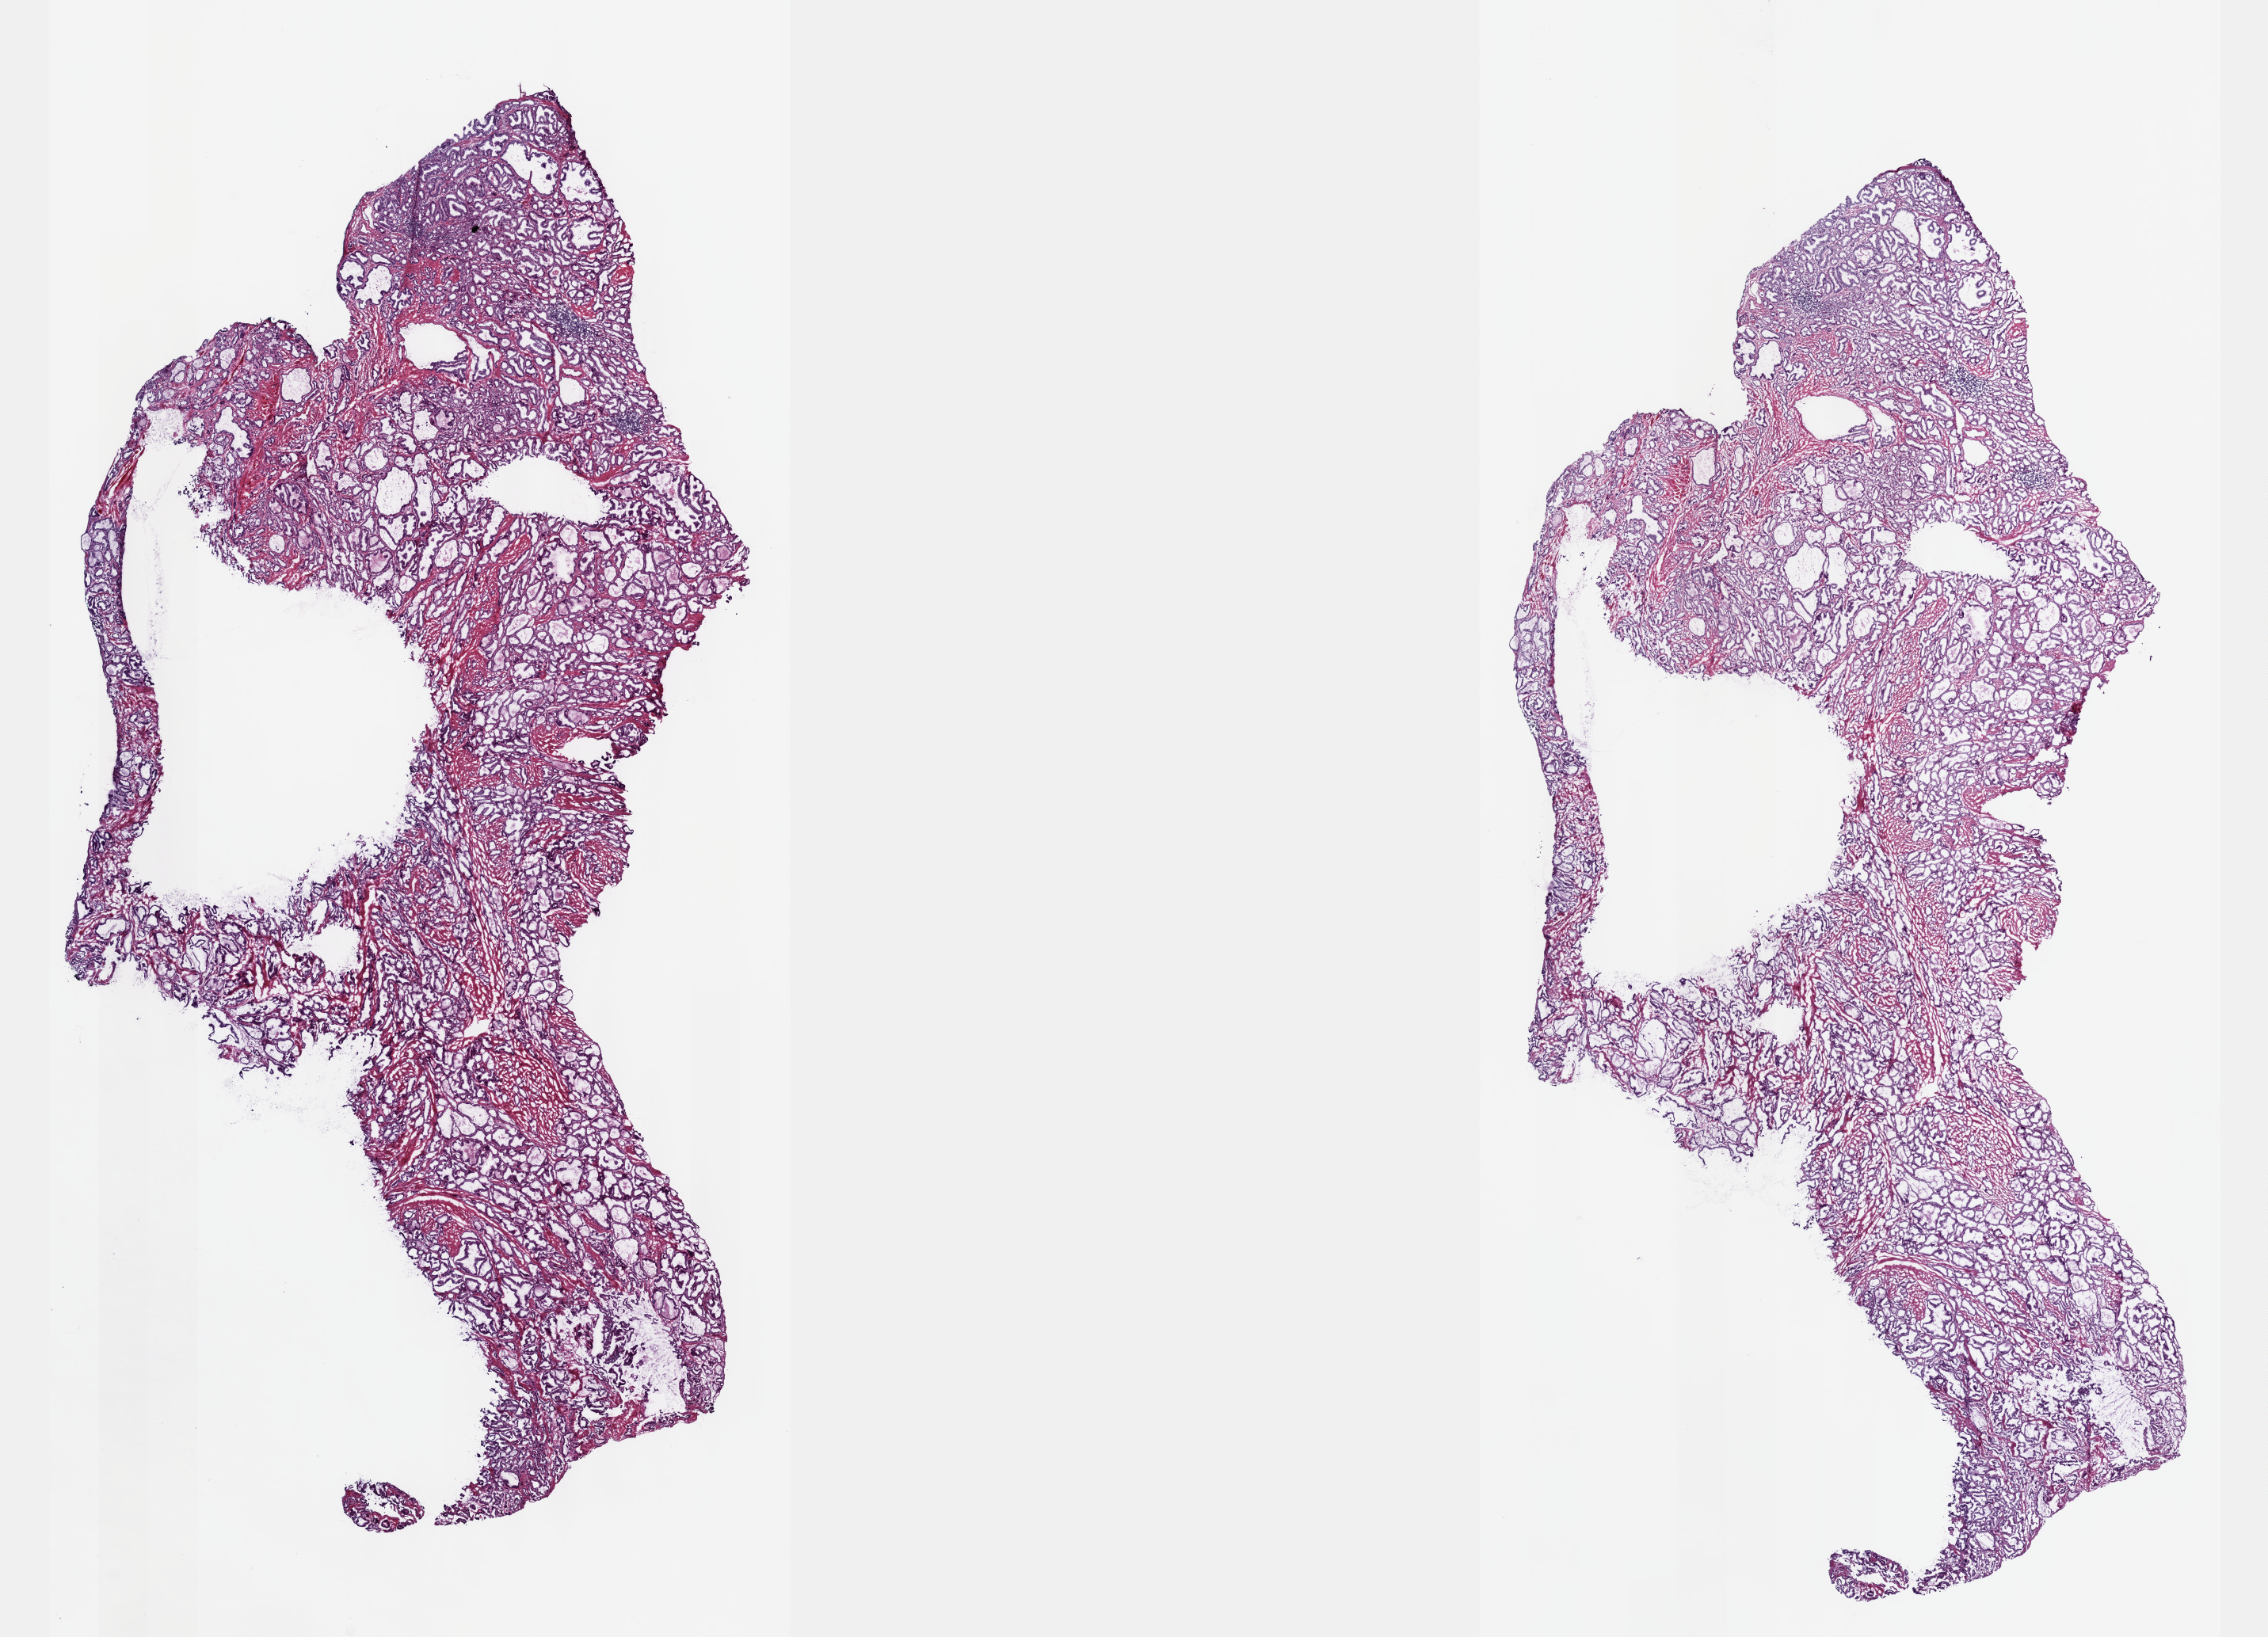
Digitized Hematoxylin and eosin (H&E) stained tissue section (whole slide) — whole scanned area (about 23.1 x 16.7 mm, acquisition: 40x scan) shown as a low-resolution overview; frozen section; primary tumour sample from the prostate. Male, age 67 years at initial diagnosis. Gleason score: 6 (3+3). Pathologist review of this section (percent, as recorded): tumour cells 80%, tumour nuclei 80%, normal cells 0%, stromal cells 20%, necrosis 0%. Infiltration values recorded for this section: lymphocyte infiltration 40%, monocyte infiltration 20%, neutrophil infiltration 20%.
• diagnosis: Adenocarcinoma, NOS (prostate gland)